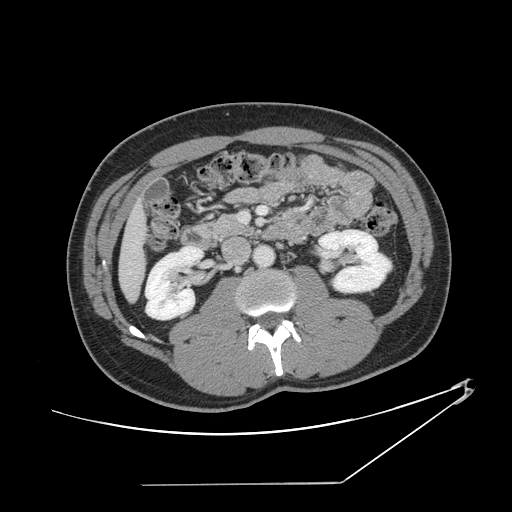
Contrast-enhanced abdominal CT, one axial slice; position 50 of 152 along the scan axis; 120 kVp; intravenous contrast given; soft-tissue window (W 400 / L 40 HU); 512 × 512 image matrix, field of view 432 × 432 mm. Male patient, age 45 years. Case-level facts recorded for this patient, not image findings: diagnosis: colorectal cancer liver metastases, imaged before liver resection; multiple liver metastases: no; largest metastasis: 1 cm.
Annotated regions visible in this slice (expert manual segmentation):
- hepatic veins: bounding box (x1, y1, x2, y2) in pixels: (133, 240, 139, 248)
- liver: (120, 208, 145, 299)
- planned liver remnant (the part of the liver to remain after resection): (120, 208, 145, 299)
- portal vein (with intrahepatic branches): (240, 206, 267, 221)